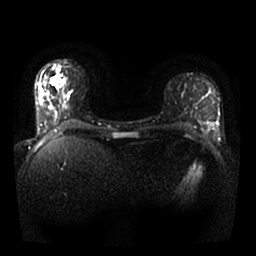
Breast MRI, one axial slice; position 10 of 25 along the scan axis; diffusion-weighted series; image 2 of 4 stored at this slice position (different b-values; order by instance number); 1.5 T; 256 × 256 image matrix, field of view 330 × 330 mm. Female patient.
Annotated regions visible in this slice (manually delineated by an expert):
- tumour on diffusion-weighted imaging: bounding box (x1, y1, x2, y2) in pixels: (50, 77, 64, 85)